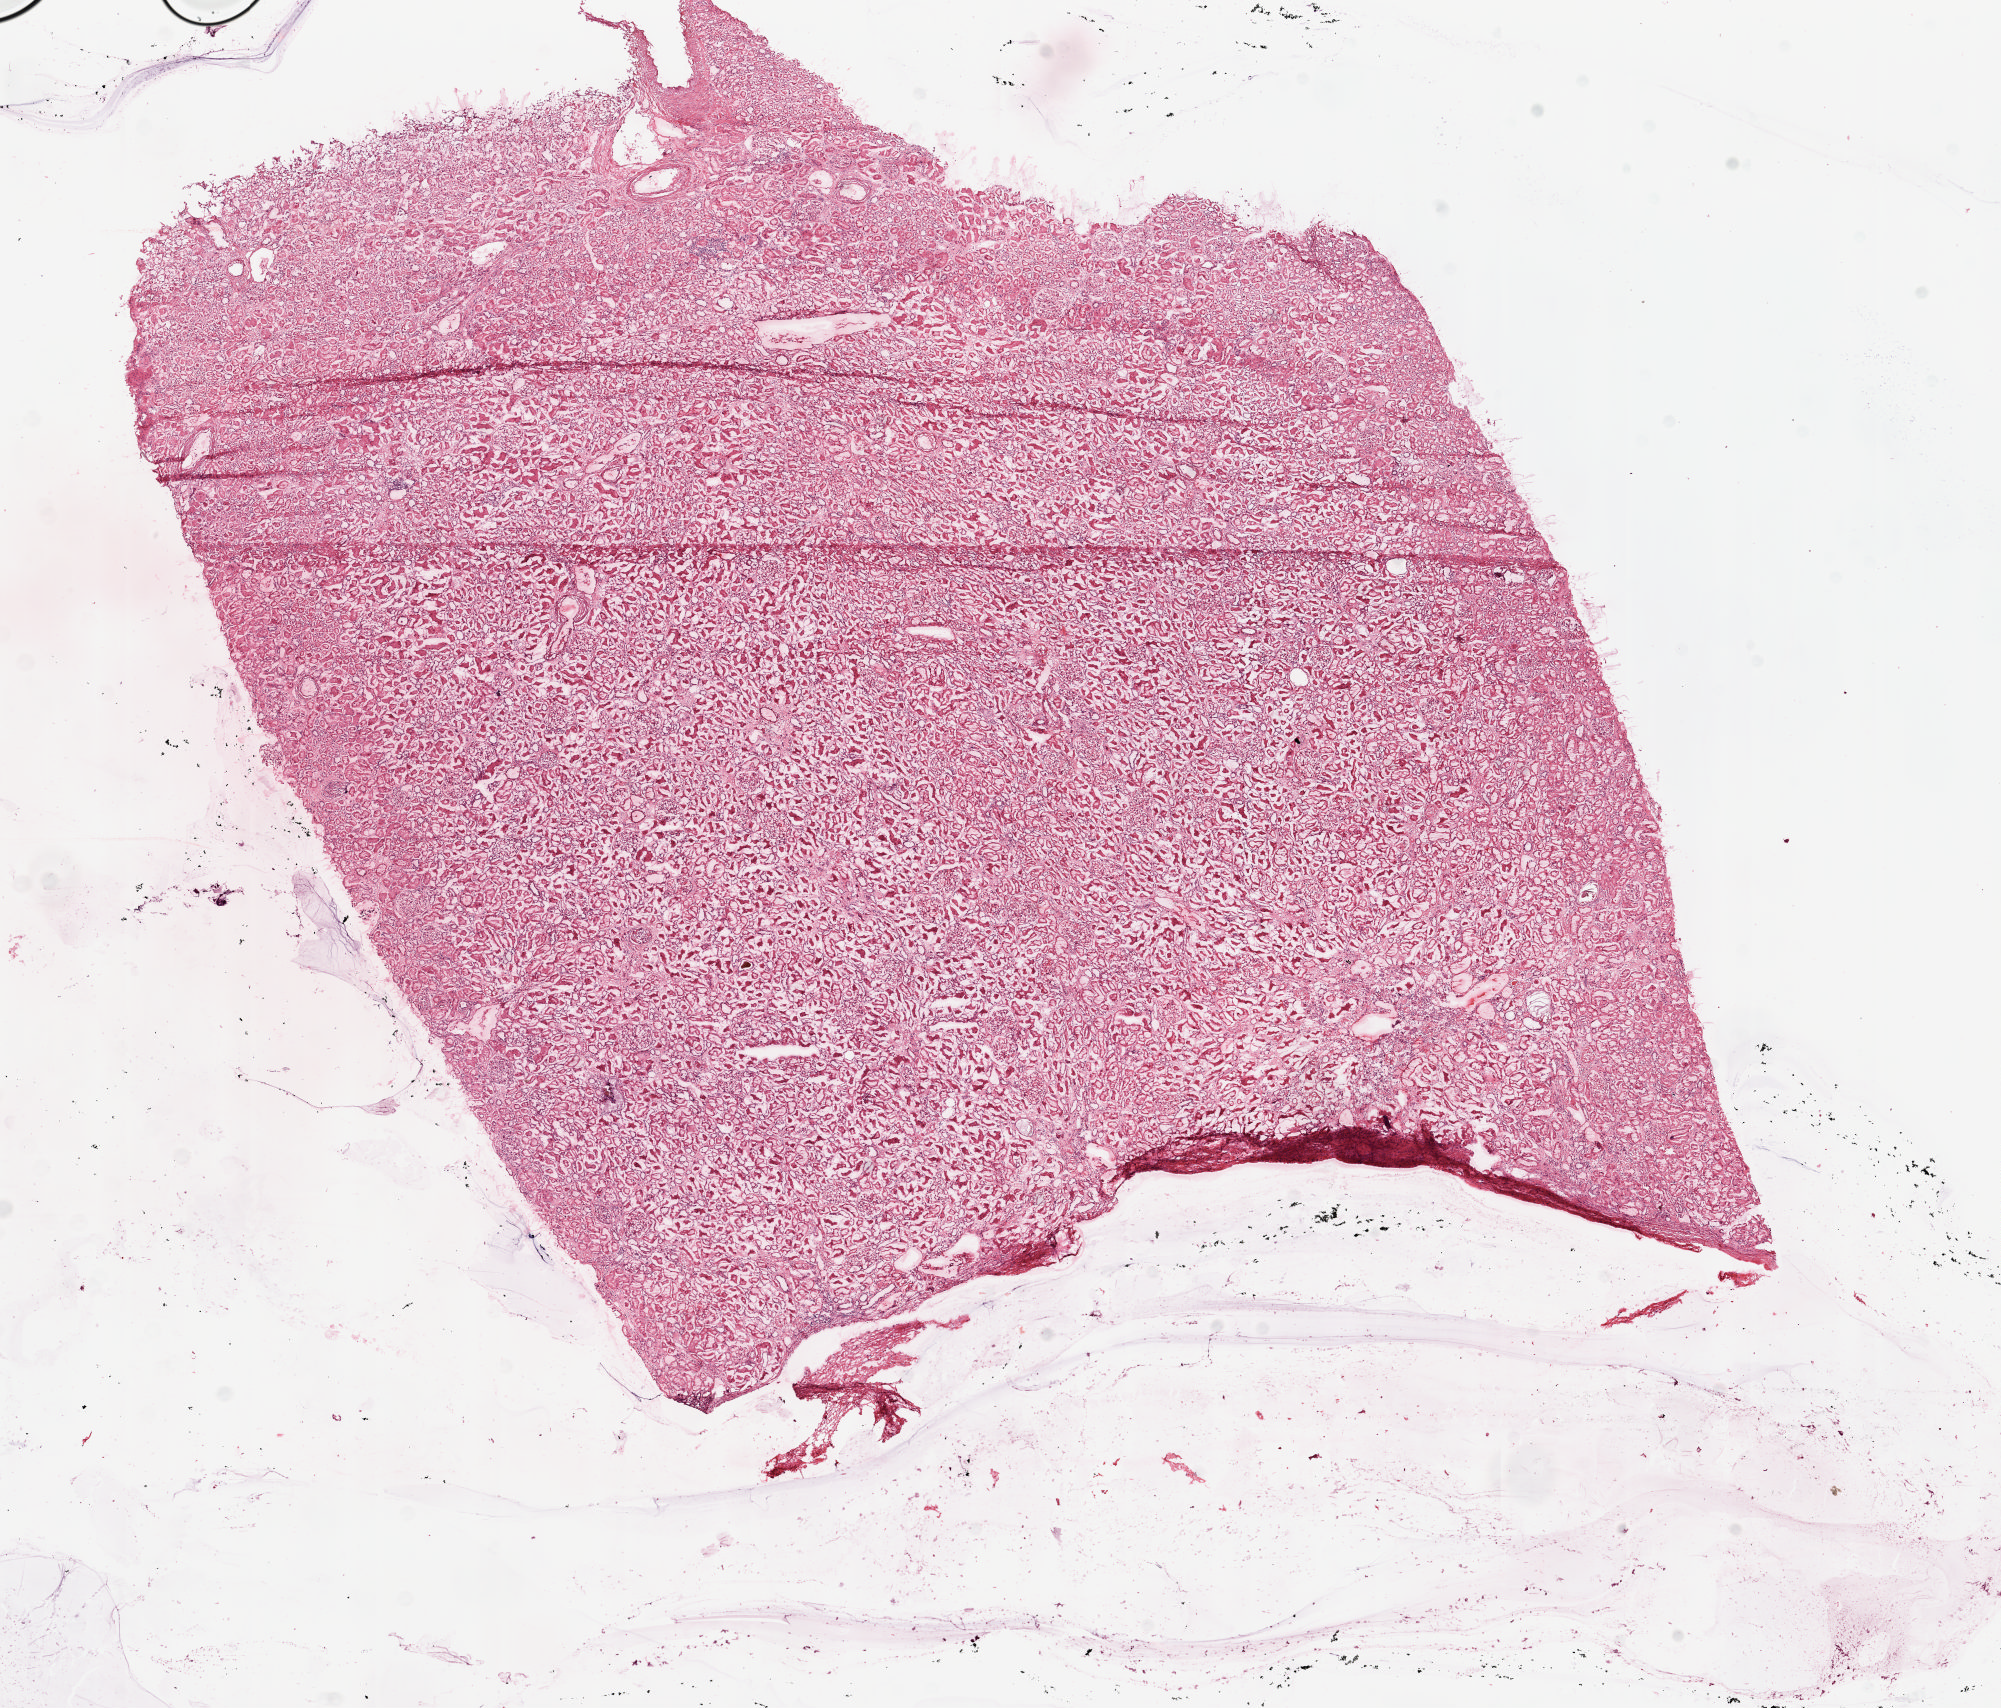
Hematoxylin and eosin (H&E) stained whole-slide image, low-resolution overview of the scanned area, about 15.9 x 13.5 mm (slide scanned at 20x); frozen section from the top of the tissue portion; sample: solid tissue normal (non-tumour tissue), kidney. Male, age 60 years at initial diagnosis.
This section: solid tissue normal sample (biorepository sample class). Patient diagnosis: Clear cell adenocarcinoma, NOS.